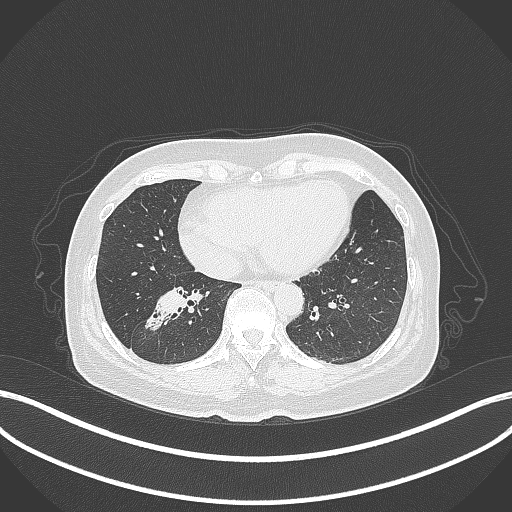
Chest CT, one axial slice; position 135 of 429 along the scan axis; 120 kVp; lung window (W 1500 / L -600 HU); 1 mm slice thickness; 512 × 512 image matrix, field of view 400 × 400 mm. Female patient, age 67 years. From the clinical record (not read from this slice): clinical TNM (as recorded): T1c N1 M0.
Outlined on this slice (bounding box drawn by a radiologist):
- lung tumour (recorded histology: adenocarcinoma): bounding box <138,283,192,333> (left, top, right, bottom; pixels)